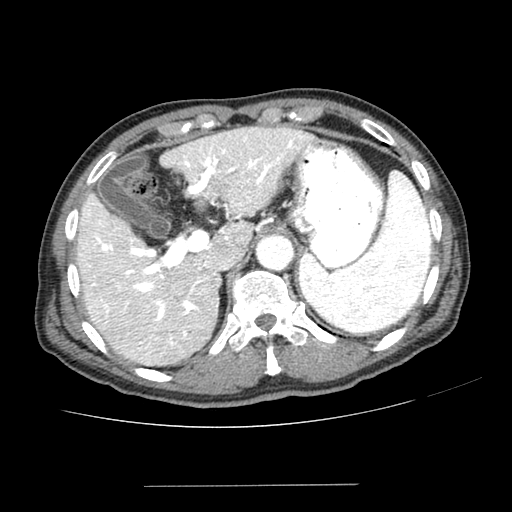
Contrast-enhanced abdominal CT (liver protocol), one axial slice; slice 161 of 187 in the series (ordered by position); reconstruction kernel SOFT; 100 kVp; one of 2 acquisitions stored at this slice position; soft-tissue window (W 400 / L 40 HU); 2.5 mm slice thickness; 512 × 512 image matrix, field of view 360 × 360 mm. From the clinical record (not read from this slice): diagnosis: hepatocellular carcinoma (patient treated with transarterial chemoembolisation; whether this scan precedes or follows treatment is not stated here); TNM stage (as recorded): Stage-I; Child-Pugh class: A; tumour differentiation: poorly differentiated.
Outlined on this slice (semi-automatic segmentation, software-assisted and operator-edited):
- liver parenchyma outside the tumour (the mass and vessels are separate outlines, so this box may not span the whole liver): bounding box (x1, y1, x2, y2) in pixels: (76, 126, 312, 364)
- liver vessels: (88, 136, 303, 345)